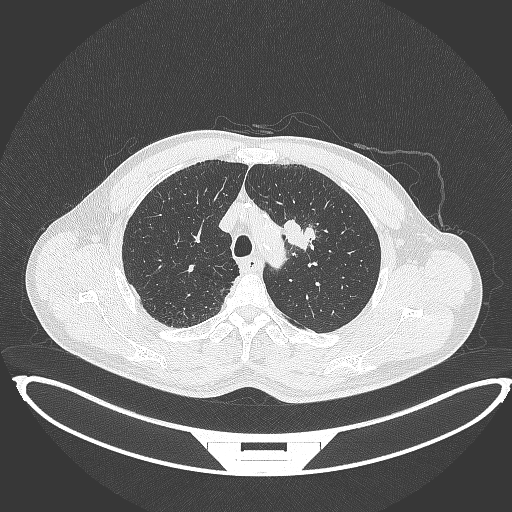
Chest CT, one axial slice; slice 337 of 395 in the series (ordered by position); 120 kVp; lung window (W 1500 / L -600 HU); 512 × 512 image matrix, field of view 457 × 457 mm. Male patient, age 60 years. From the clinical record (not read from this slice): clinical TNM (as recorded): T2a N0 M0; histopathological grade: G1-G2.
Annotated regions visible in this slice (bounding box drawn by a radiologist):
- lung tumour (recorded histology: squamous cell carcinoma): bounding box <281,218,317,252> (left, top, right, bottom; pixels)